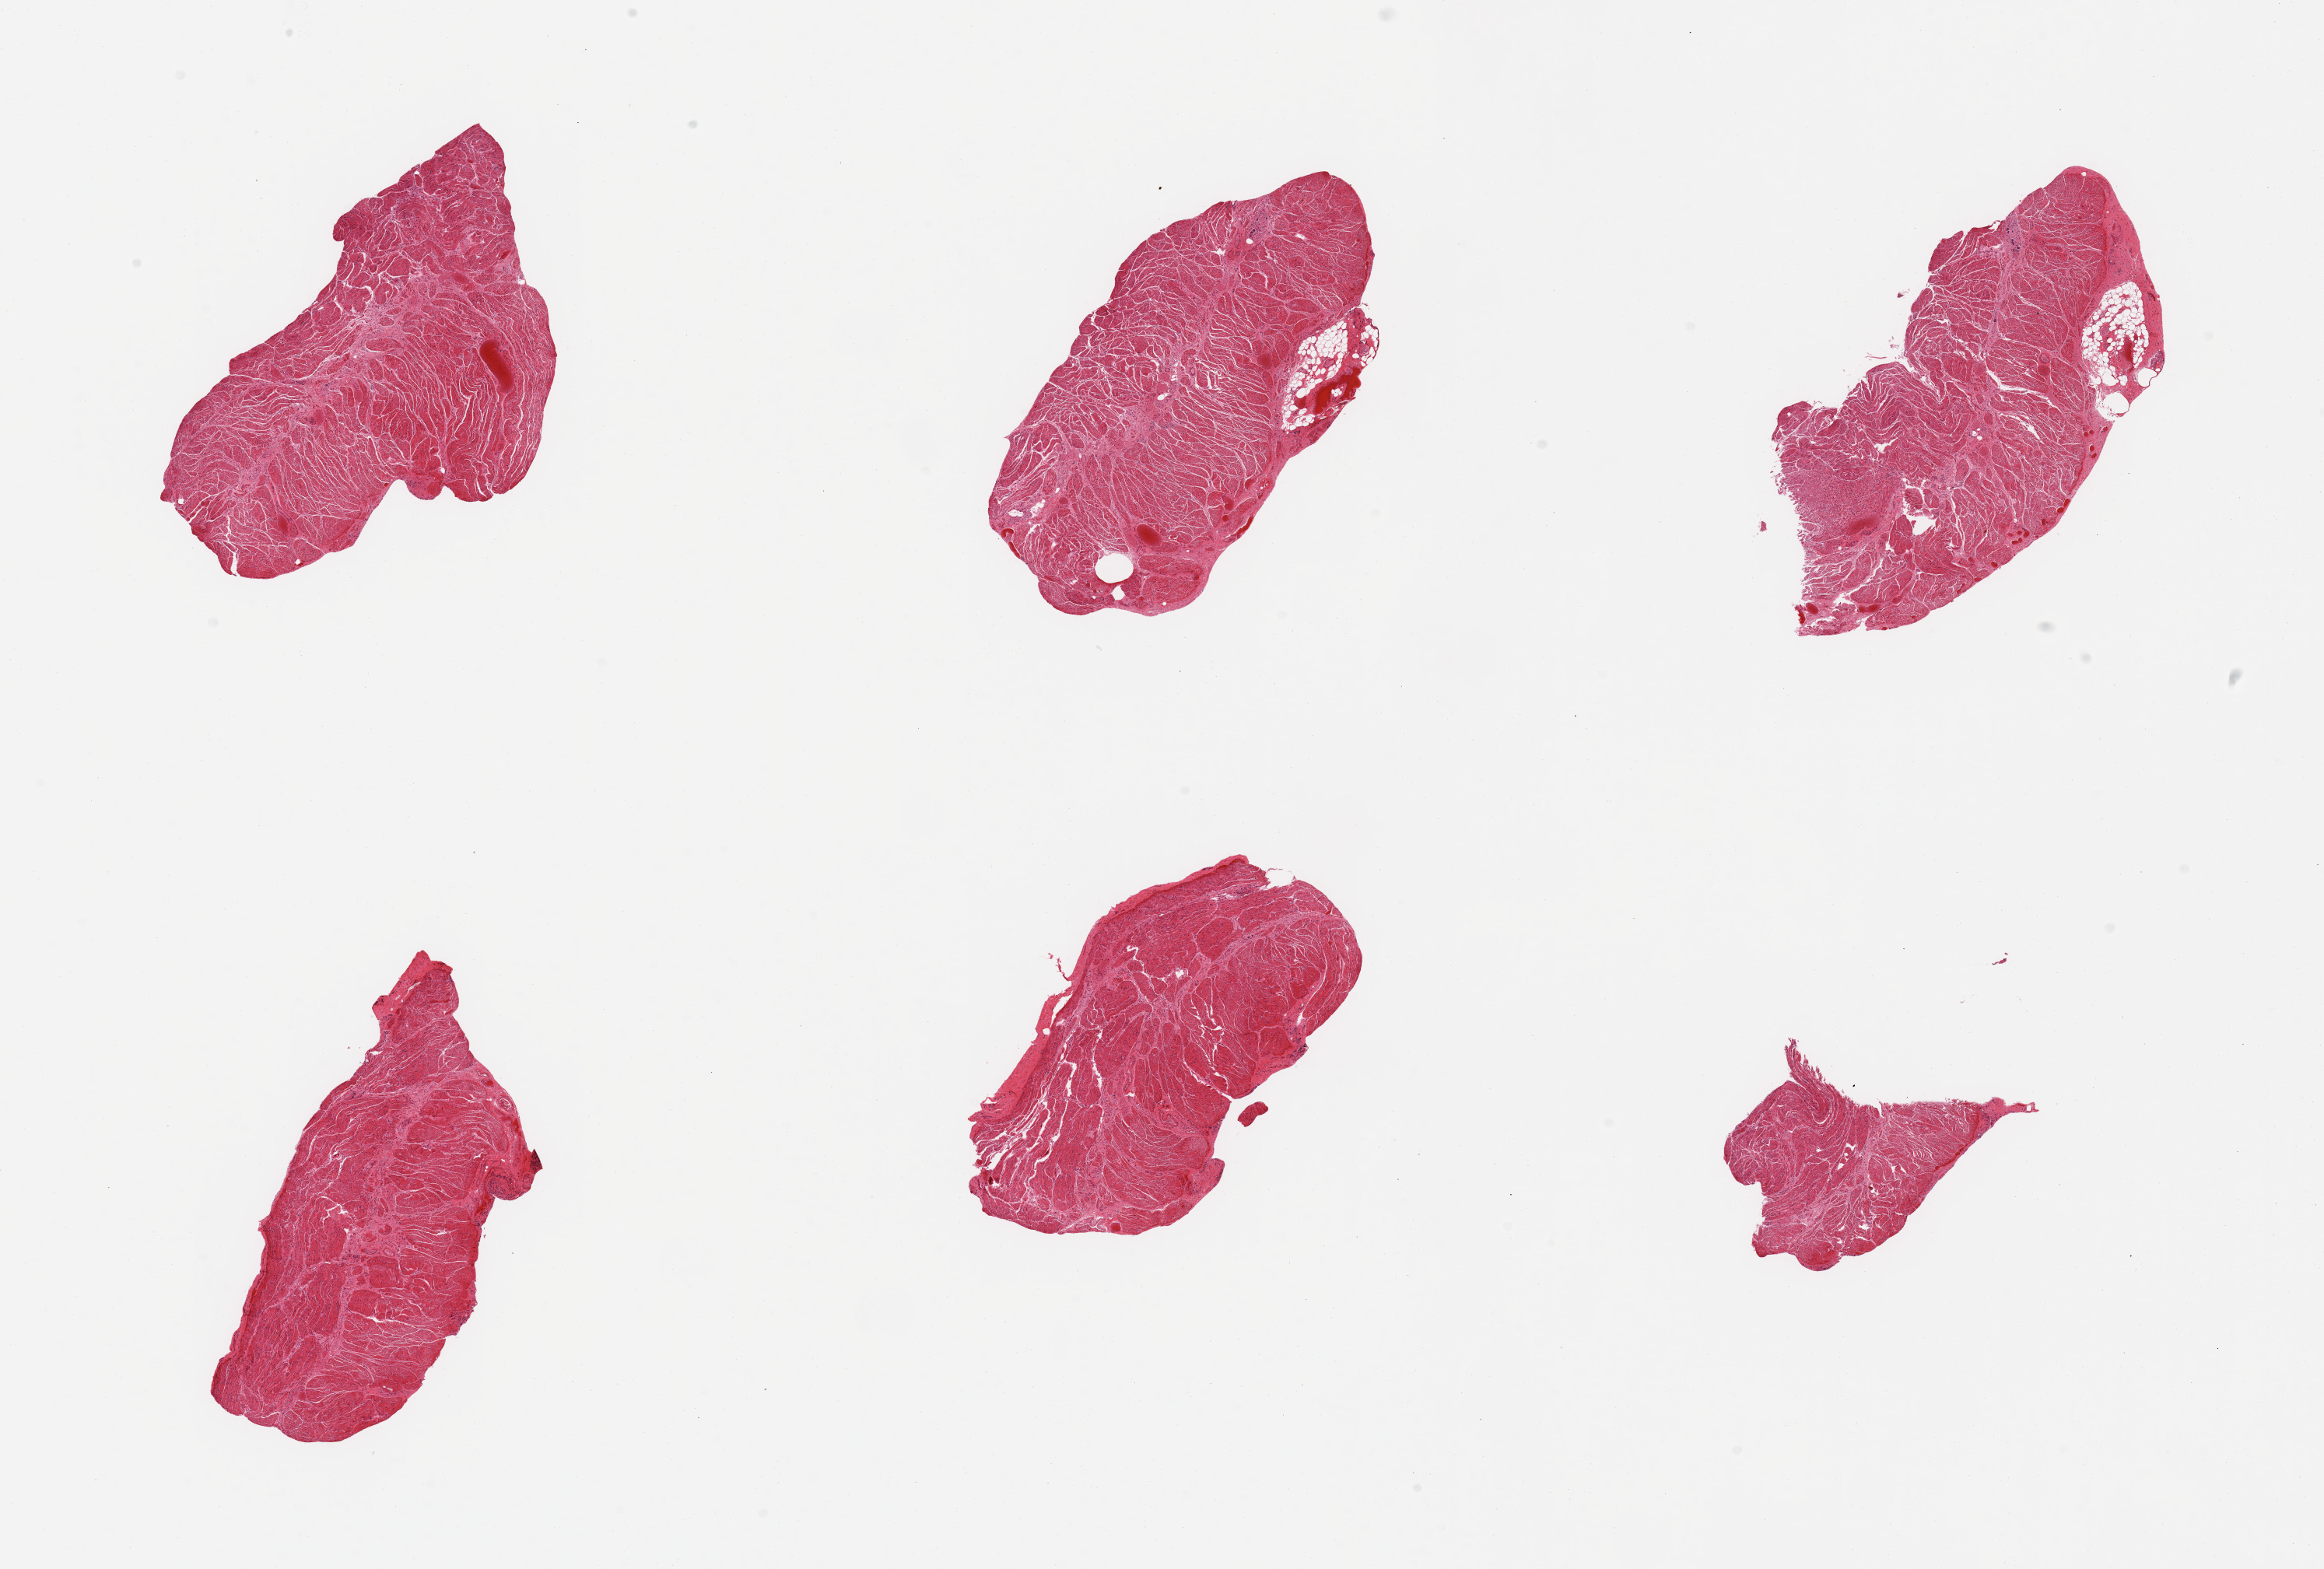
Digitized hematoxylin and eosin (H&E)-stained section, a low-resolution overview of the entire scanned area, about 23.6 x 16.0 mm, PAXgene-fixed paraffin-embedded (PFPE) section, sampled site (target tissue): gastroesophageal junction, tissue donor sample. Donor sex: male.
Pathologist's review note for this sample: 6 pieces; target muscularis, 2 of 6 with attached fat.